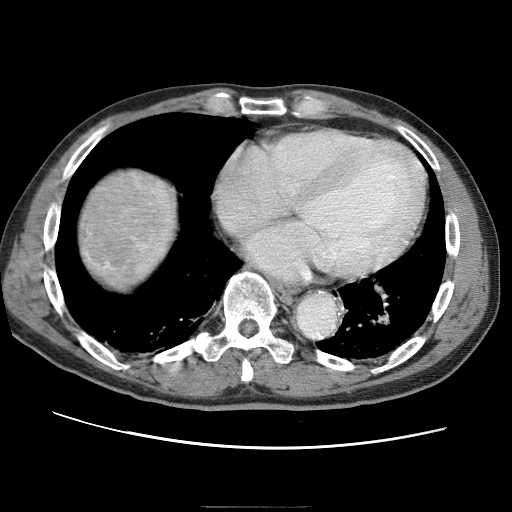
Contrast-enhanced abdominal CT (liver protocol), one axial slice; position 68 of 75 along the scan axis; 120 kVp; one of 2 acquisitions stored at this slice position; soft-tissue window (W 400 / L 40 HU); 2.5 mm slice thickness; 512 × 512 image matrix. From the clinical record (not read from this slice): diagnosis: hepatocellular carcinoma (patient treated with transarterial chemoembolisation; whether this scan precedes or follows treatment is not stated here); TNM stage (as recorded): Stage-II; Child-Pugh class: A.
Annotated regions visible in this slice (semi-automatically segmented with operator editing):
- liver parenchyma outside the tumour (the mass and vessels are separate outlines, so this box may not span the whole liver): bounding box (x1, y1, x2, y2) in pixels: (72, 160, 192, 303)
- mass: (73, 165, 166, 283)